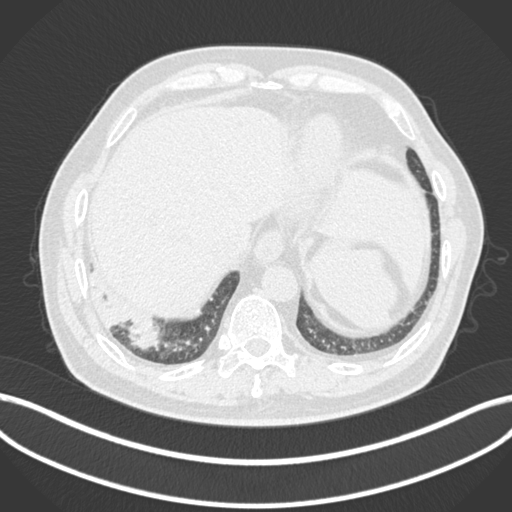
Chest CT, one axial slice. Position 19 of 200 along the scan axis. Reconstruction kernel B30f. 120 kVp. Lung window (W 1500 / L -600 HU). 512 × 512 image matrix, field of view 400 × 400 mm. Male patient, age 59 years.
Annotated regions visible in this slice (bounding box drawn by a radiologist):
- lung tumour (recorded histology: adenocarcinoma): bounding box <121,316,166,356> (left, top, right, bottom; pixels)